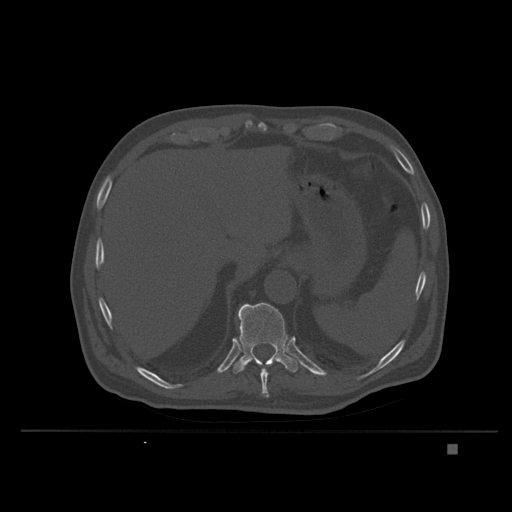
CT including the spine, one axial slice. Slice 183 of 435 in the series (ordered by position). Bone window (W 1800 / L 400 HU). 1.5 mm slice thickness. 512 × 512 image matrix. Male patient, age 73 years. Case-level facts recorded for this patient, not image findings: primary cancer: skin.
Outlined on this slice (semi-automatically segmented with operator editing):
- T10 vertebra: bounding box [x1, y1, x2, y2] px = [259, 364, 268, 394]
- T11 vertebra: [232, 303, 298, 374]
- T9 vertebra: [262, 391, 269, 398]